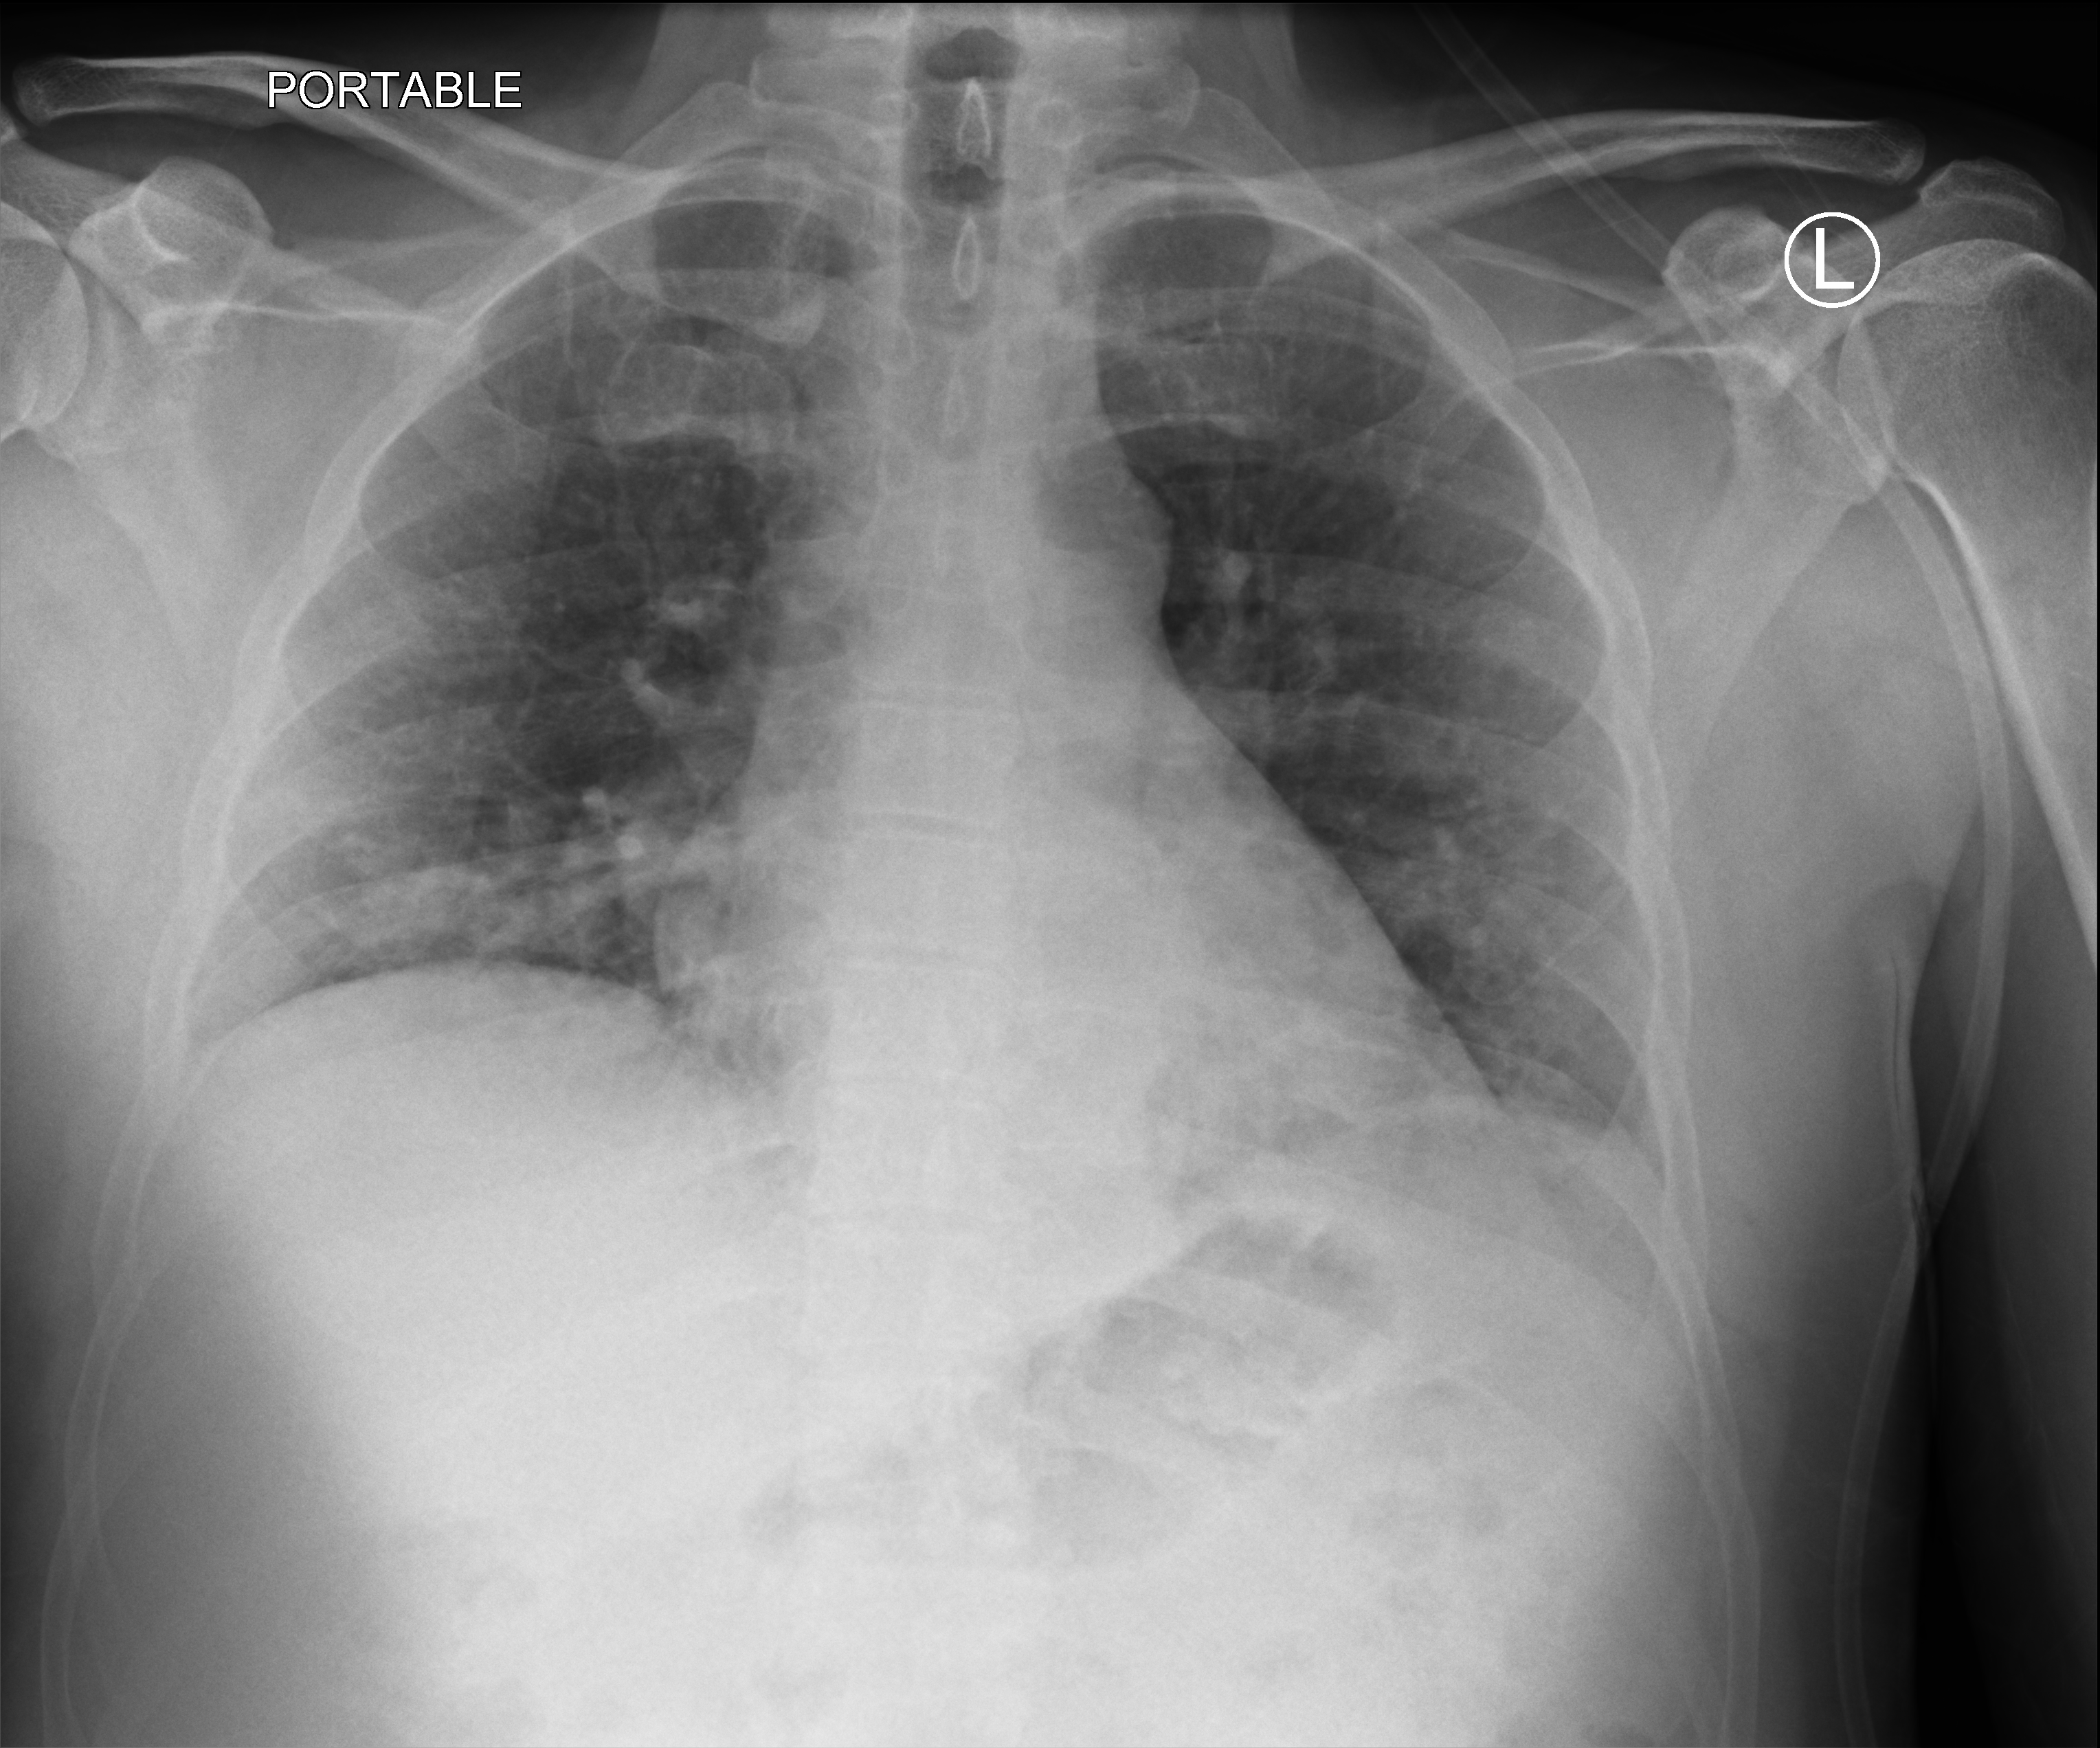
Chest X-ray (portable). Patient hospitalised with COVID-19; male, aged 18–59 years.
Hospital-stay facts (about this admission, not read from this image; timing relative to this image not recorded): admitted to intensive care during this hospital stay: no; mechanically ventilated during this hospital stay: no.